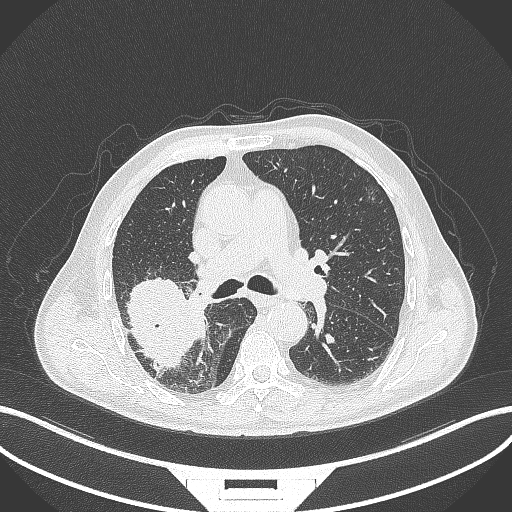
Chest CT, one axial slice; slice 250 of 429 in the series (ordered by position); reconstruction kernel B70f; lung window (W 1500 / L -600 HU); 1 mm slice thickness; 512 × 512 image matrix, field of view 400 × 400 mm. Male patient, age 72 years. Case-level facts recorded for this patient, not image findings: clinical TNM (as recorded): T3 N2 M0.
Annotated regions visible in this slice (bounding box drawn by a radiologist):
- lung tumour (recorded histology: adenocarcinoma): box from (x=120, y=274) to (x=200, y=372) px